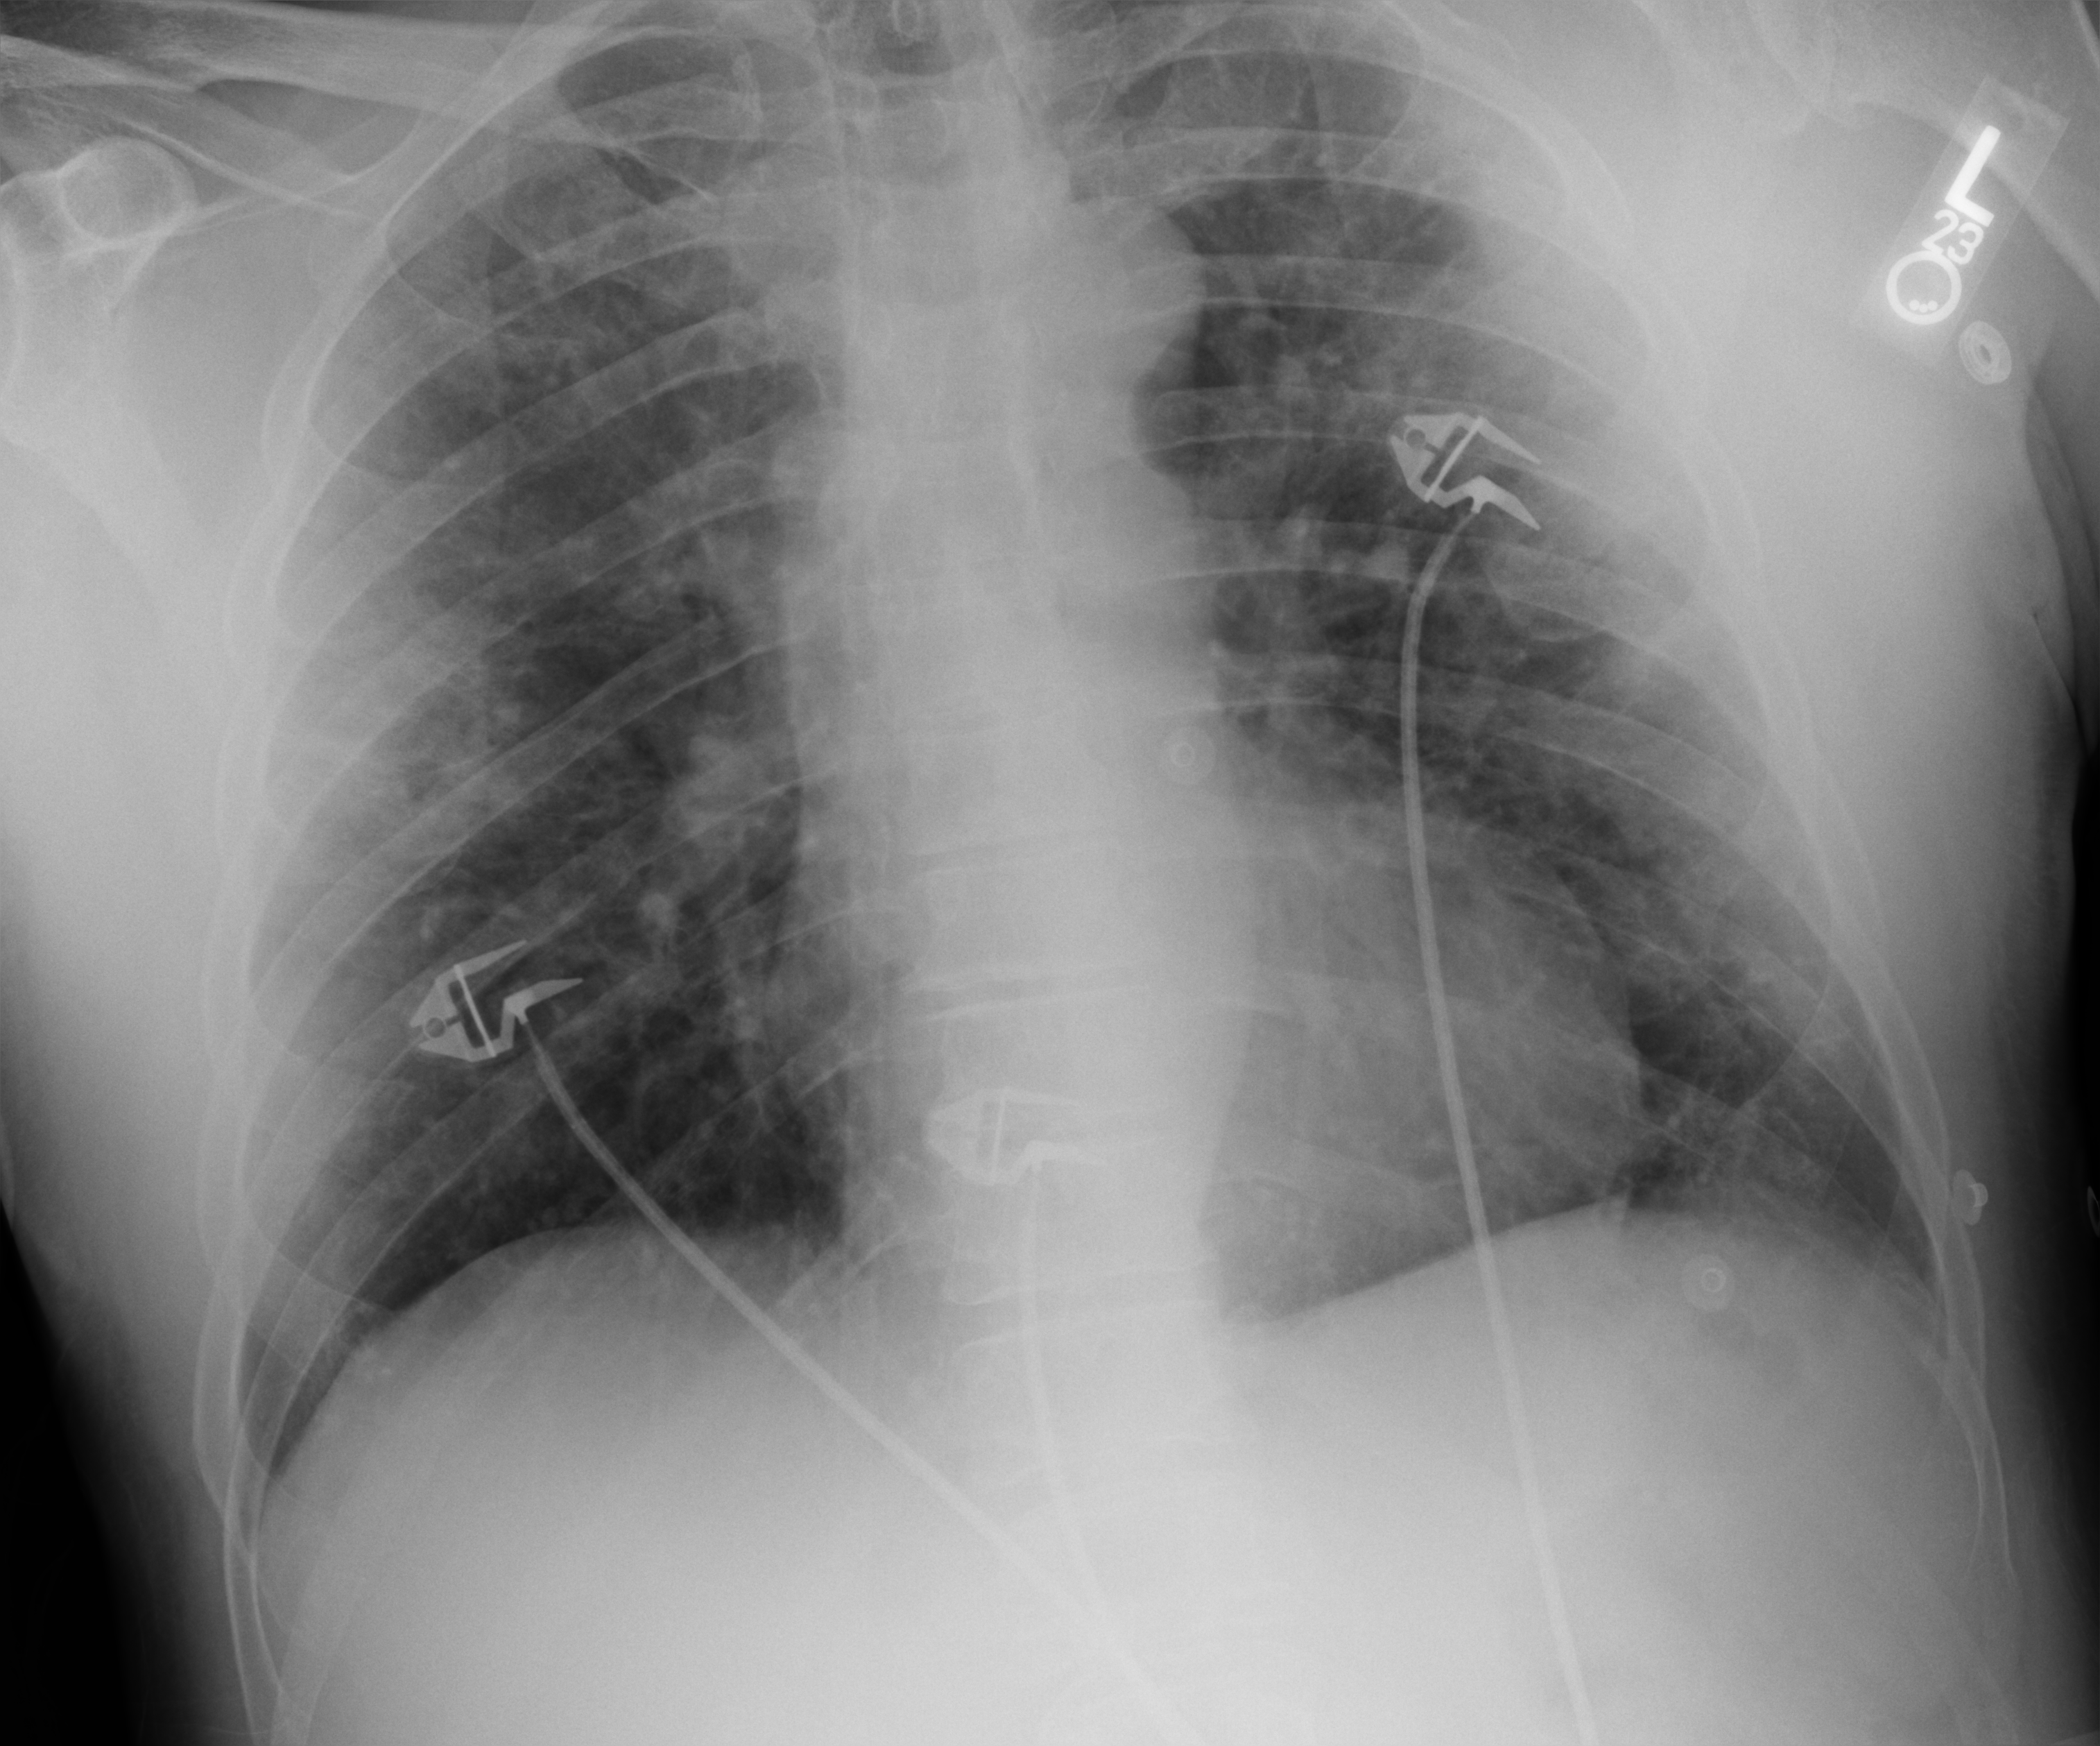
Portable chest radiograph. Male patient hospitalised with COVID-19, age 18–59 years.
From the hospital-stay record, not from the radiograph (when in the stay this image was taken is not recorded): hypertension (admission record): no.